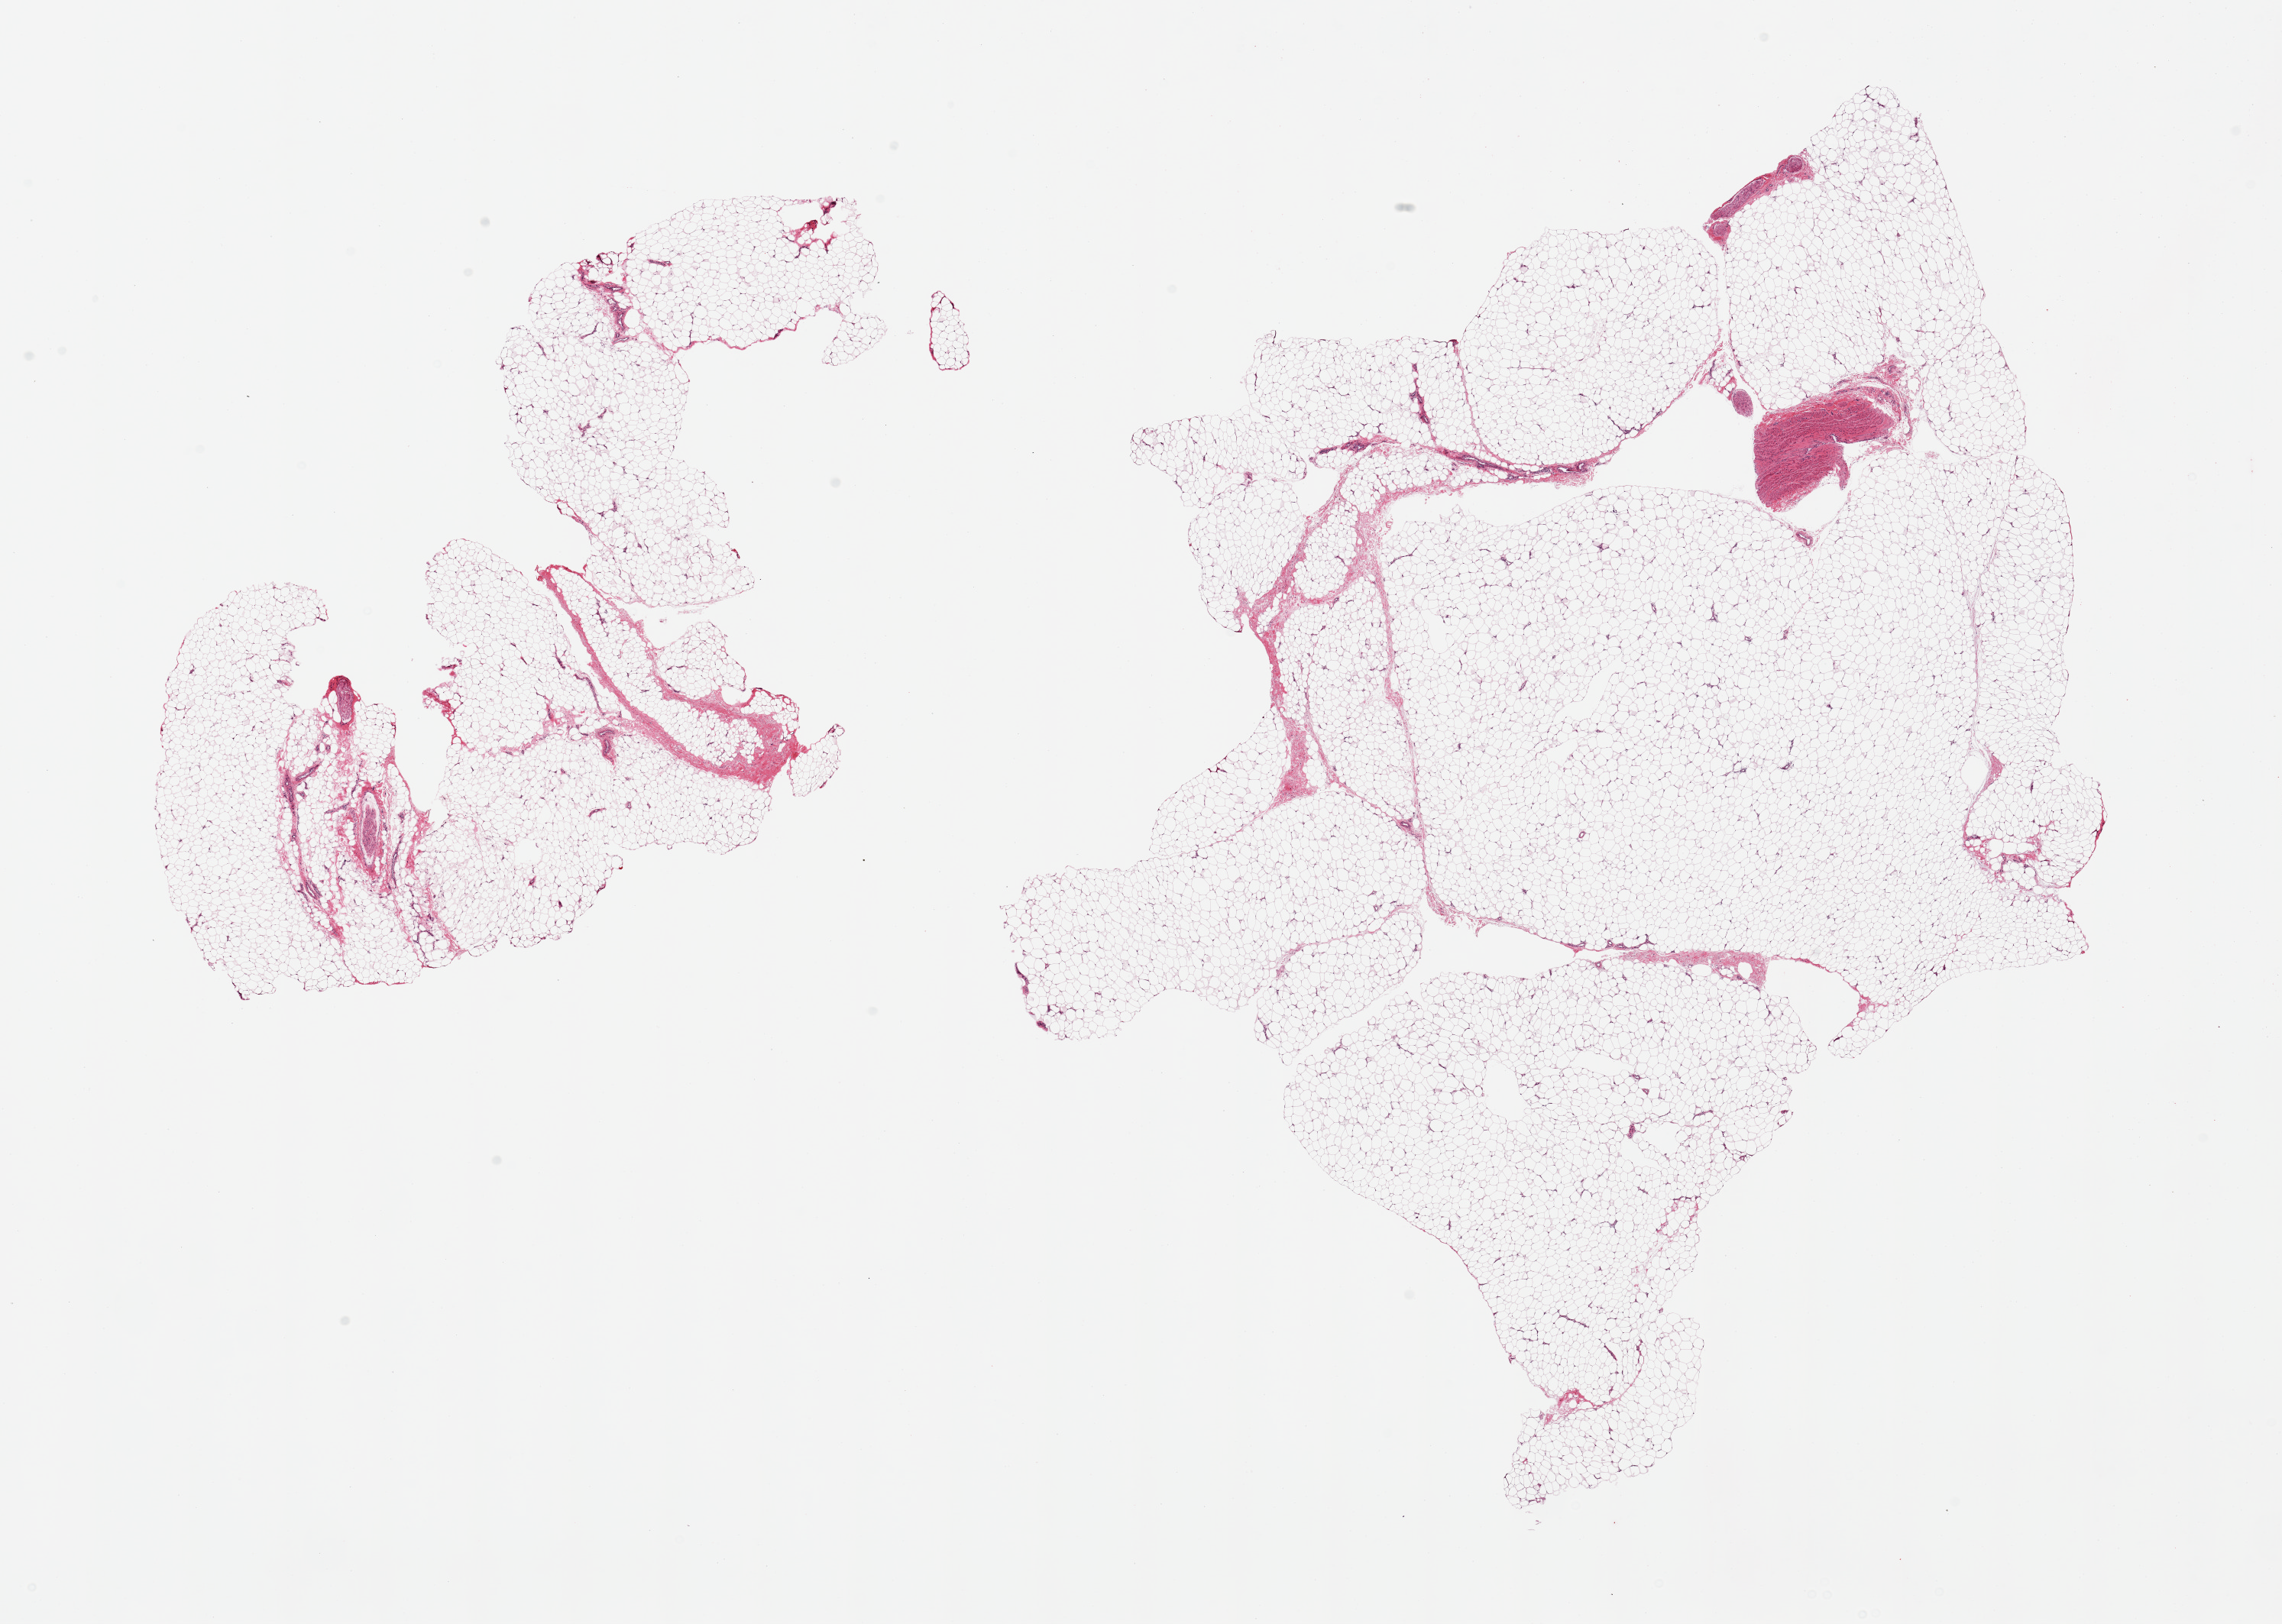
Hematoxylin and eosin (H&E) whole-slide image, whole scanned area (about 23.6 x 16.8 mm) shown as a low-resolution overview. PAXgene-fixed, paraffin-embedded tissue. Sampled site (target tissue): adipose tissue. Tissue donor sample. Donor: female.
• reviewer comment on this tissue sample: 2 pieces; fat with small portion of nerve and vessel wall